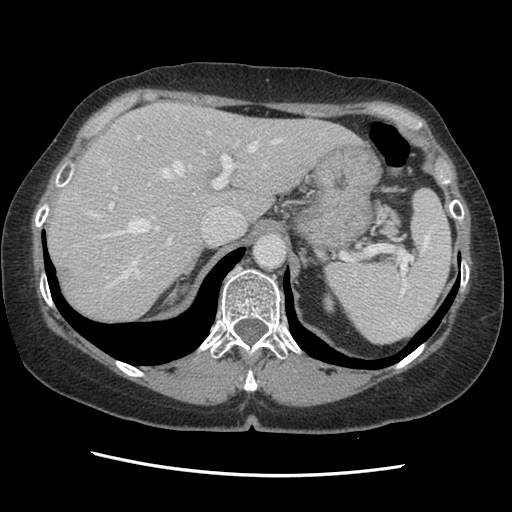
Contrast-enhanced abdominal CT, one axial slice. Slice 100 of 141 in the series (ordered by position). 120 kVp. Soft-tissue window (W 400 / L 40 HU). 512 × 512 image matrix, field of view 330 × 330 mm. Female patient, age 61 years. From the clinical record (not read from this slice): diagnosis: colorectal cancer liver metastases, imaged before liver resection; multiple liver metastases: no; largest metastasis: 2.4 cm; disease in both lobes: no.
Annotated regions visible in this slice (outlined manually by an expert reader):
- hepatic veins: bounding box <74,116,282,289> (left, top, right, bottom; pixels)
- liver: <47,104,354,325>
- planned liver remnant (the part of the liver to remain after resection): <47,104,355,325>
- portal vein (with intrahepatic branches): <109,135,239,244>